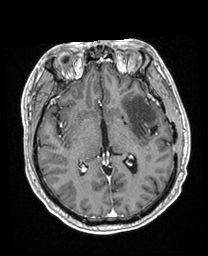
Brain MRI from a brain-tumour surgery series, one axial slice. Position 110 of 208 along the scan axis. T1-weighted post-contrast. 208 × 256 image matrix, field of view 211 × 260 mm. From the clinical record (not read from this slice): histopathology: Astrocytoma; WHO grade: 3; IDH mutation: yes; tumour location: Left Insular.
Outlined on this slice (expert manual segmentation):
- previous resection cavity: bounding box <150,125,158,136> (left, top, right, bottom; pixels)